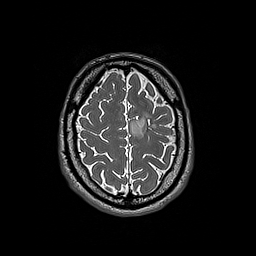
Brain MRI from a brain-tumour surgery series, one axial slice; position 50 of 192 along the scan axis; 1 mm slice thickness; 256 × 256 image matrix, field of view 250 × 250 mm. Case-level facts recorded for this patient, not image findings: histopathology: Oligodendroglioma; WHO grade: 3; IDH mutation: yes; tumour location: Left Frontal.
Structures marked on this image (manually delineated by an expert):
- tumour: box from (x=130, y=112) to (x=155, y=137) px